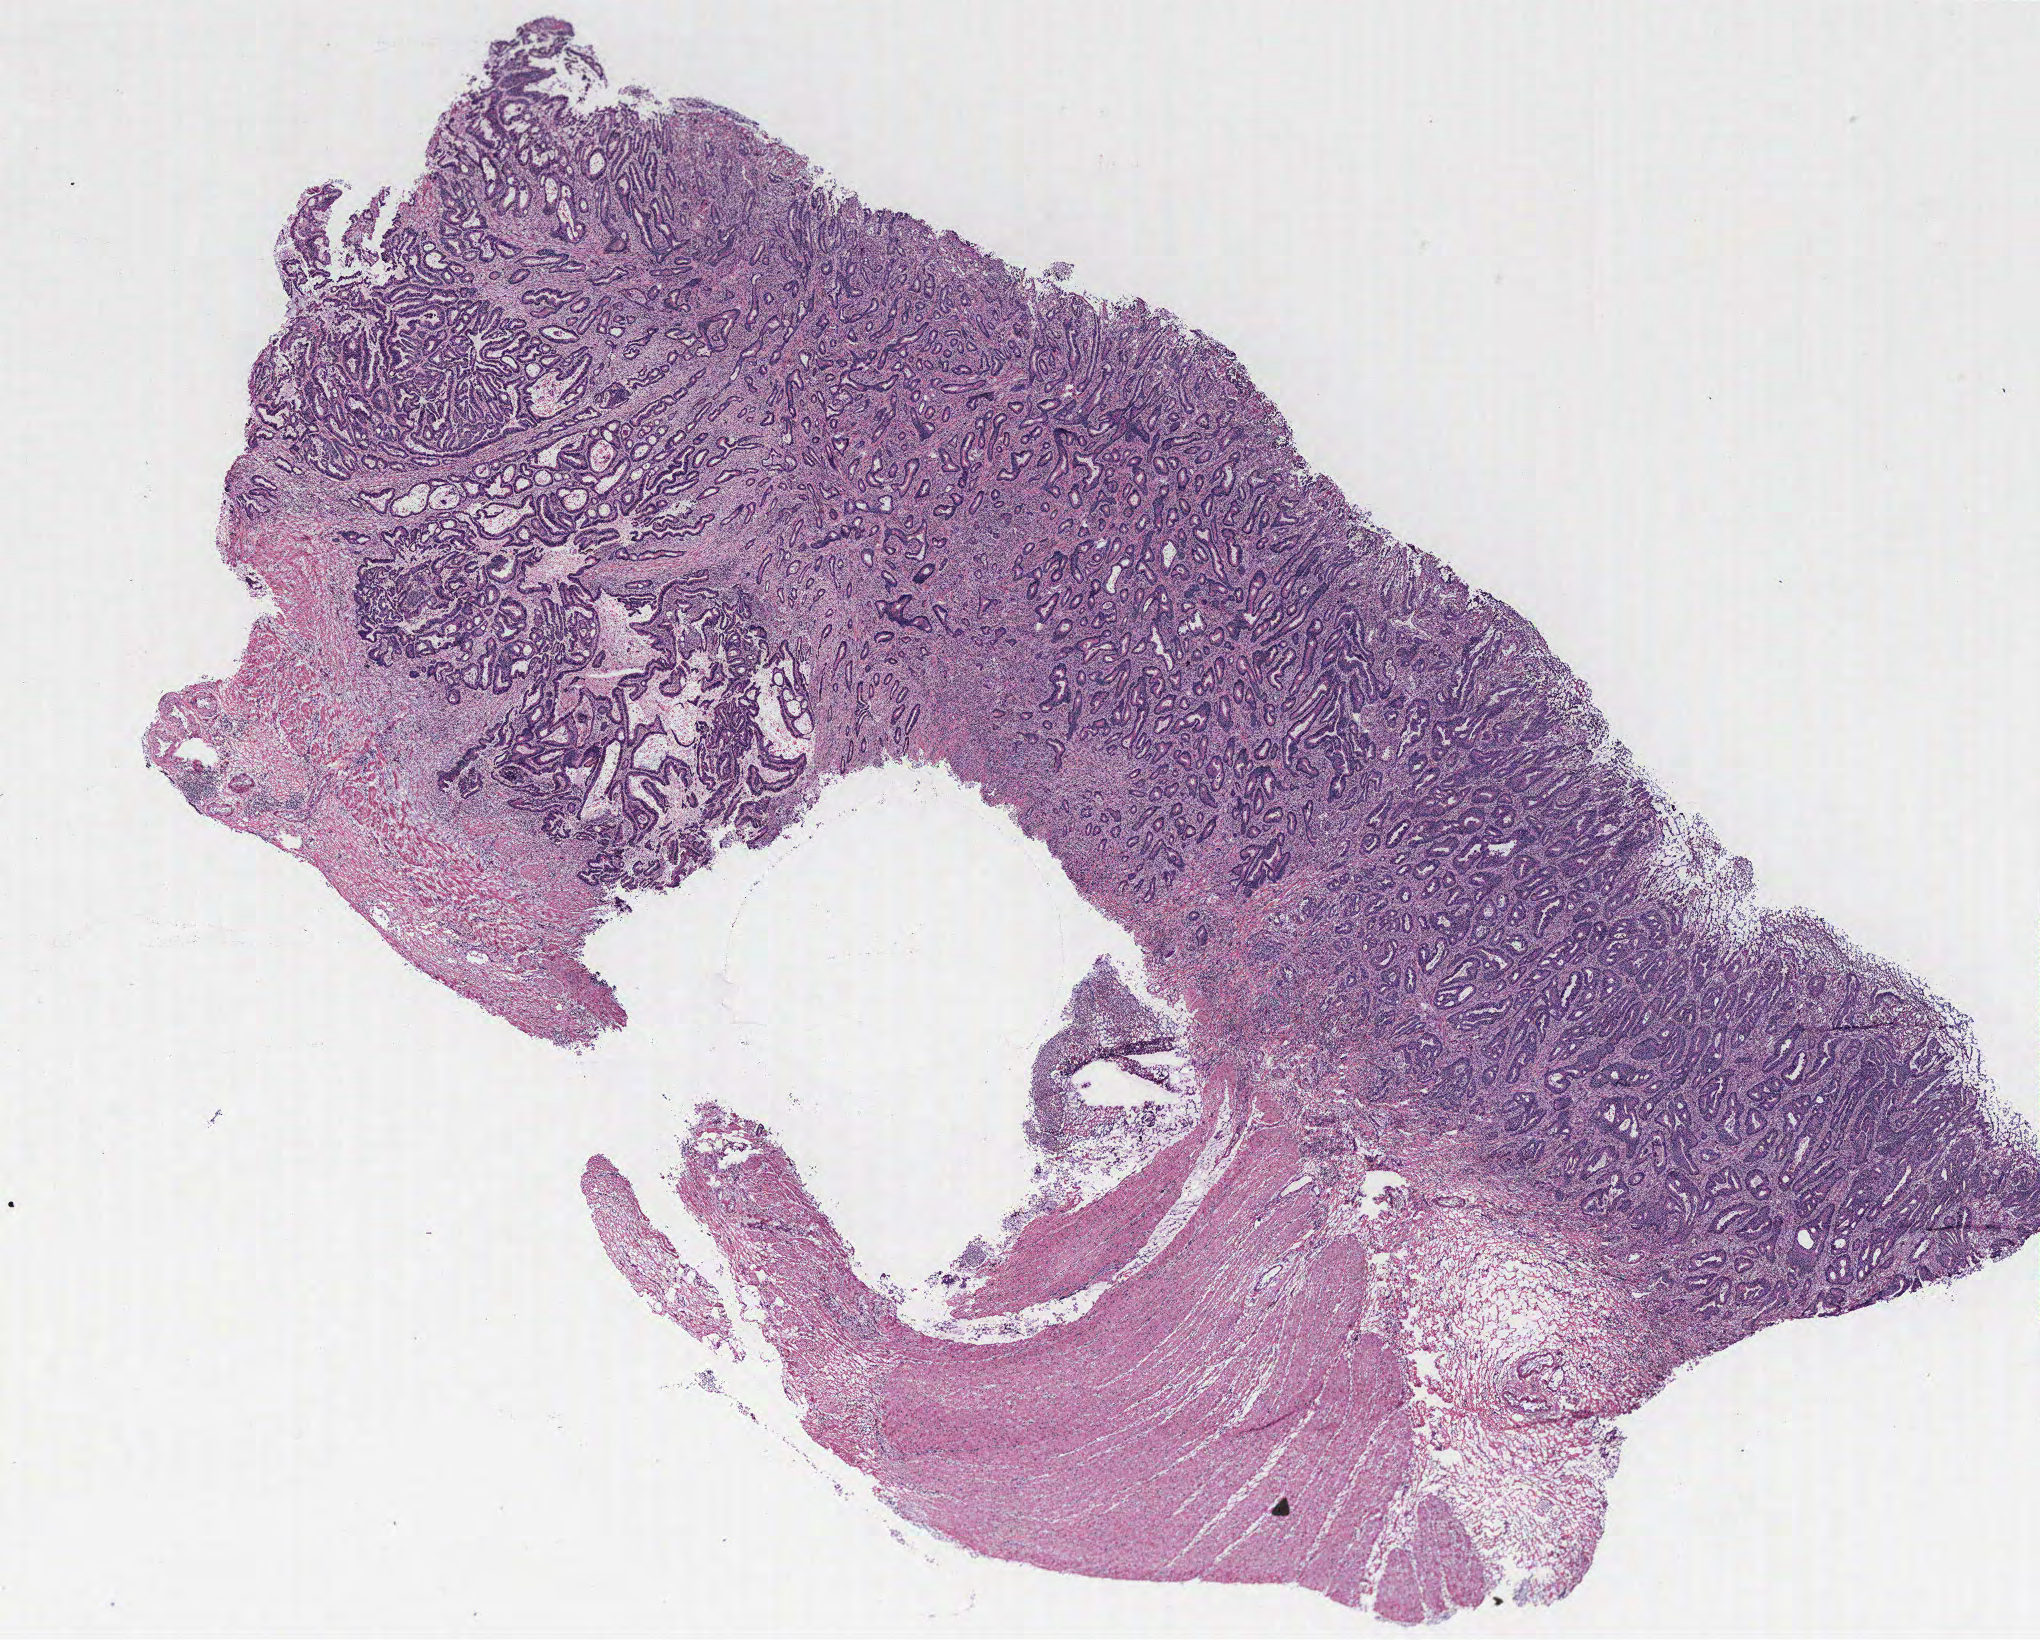
Whole-slide histology image, H&E-stained — a low-resolution overview of the entire scanned area, about 16.3 x 13.1 mm (acquisition: 40x scan). Colon, tissue type not recorded. Patient sex: female.
* patient diagnosis: Adenocarcinoma, NOS